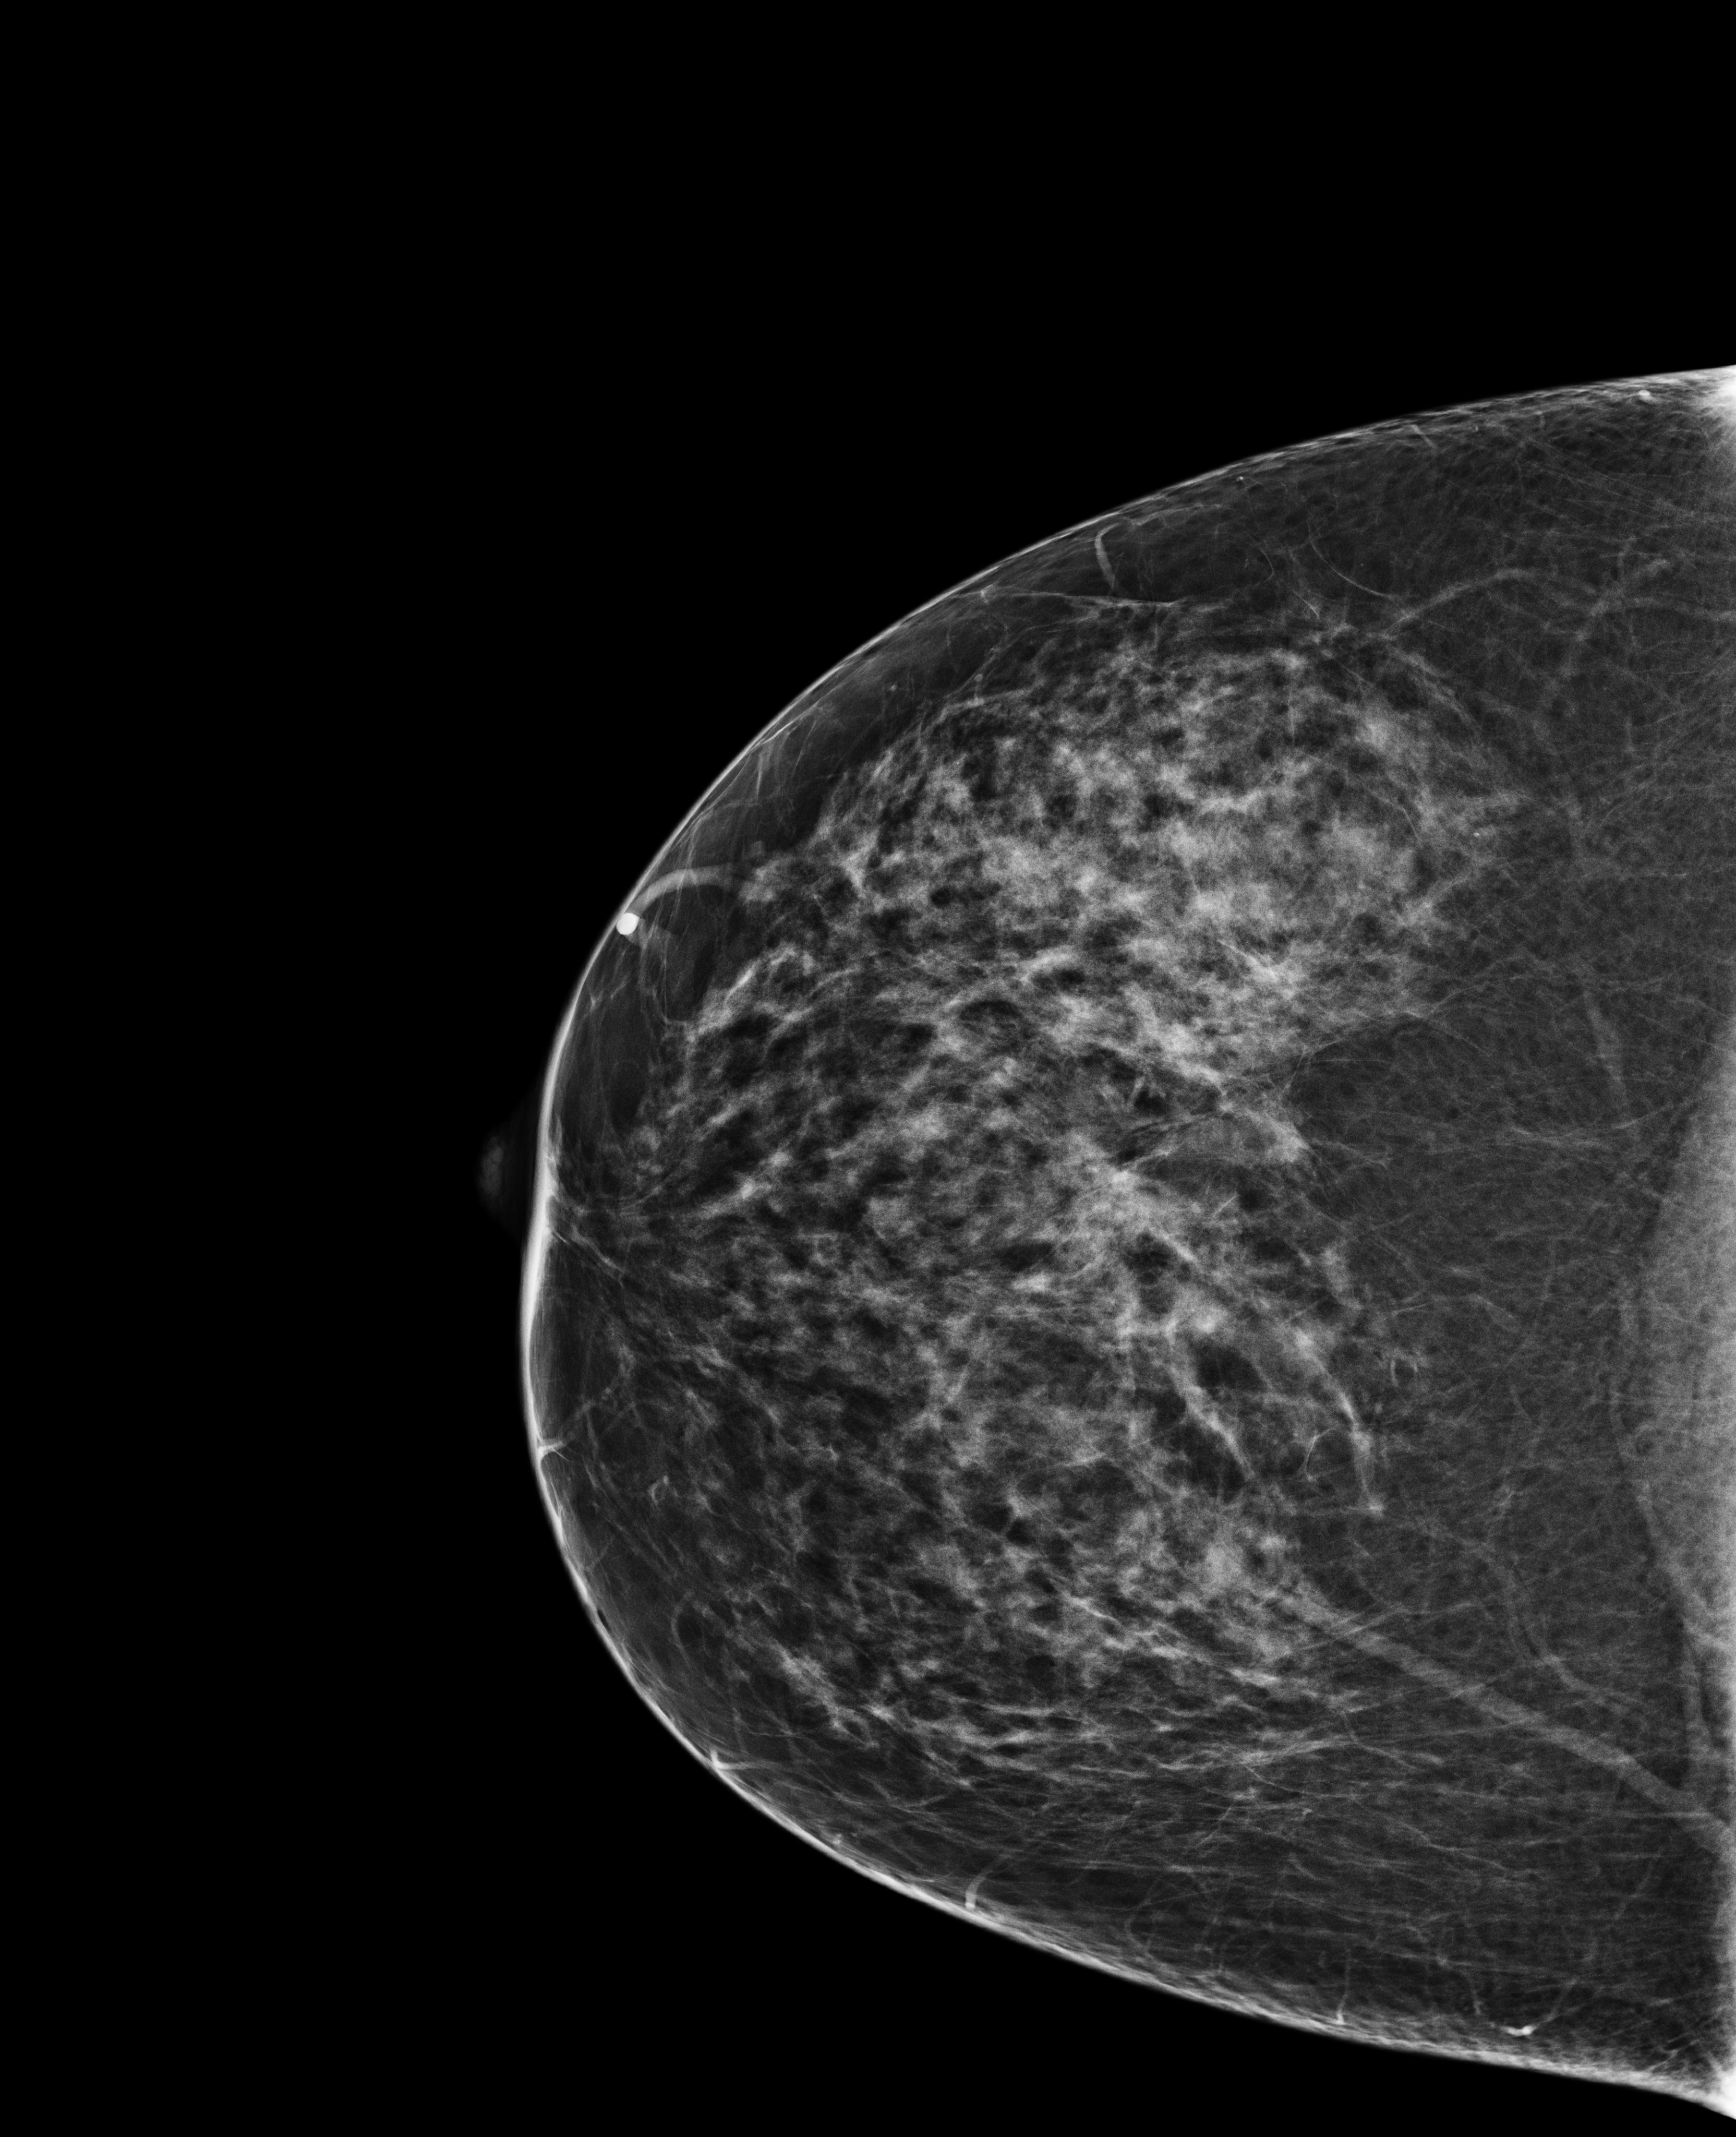
Screening examination, compressed breast thickness 67 mm. Patient: female, 51 years.
Image type: full-field digital mammogram. Breast: right. Projection: cranio-caudal projection.